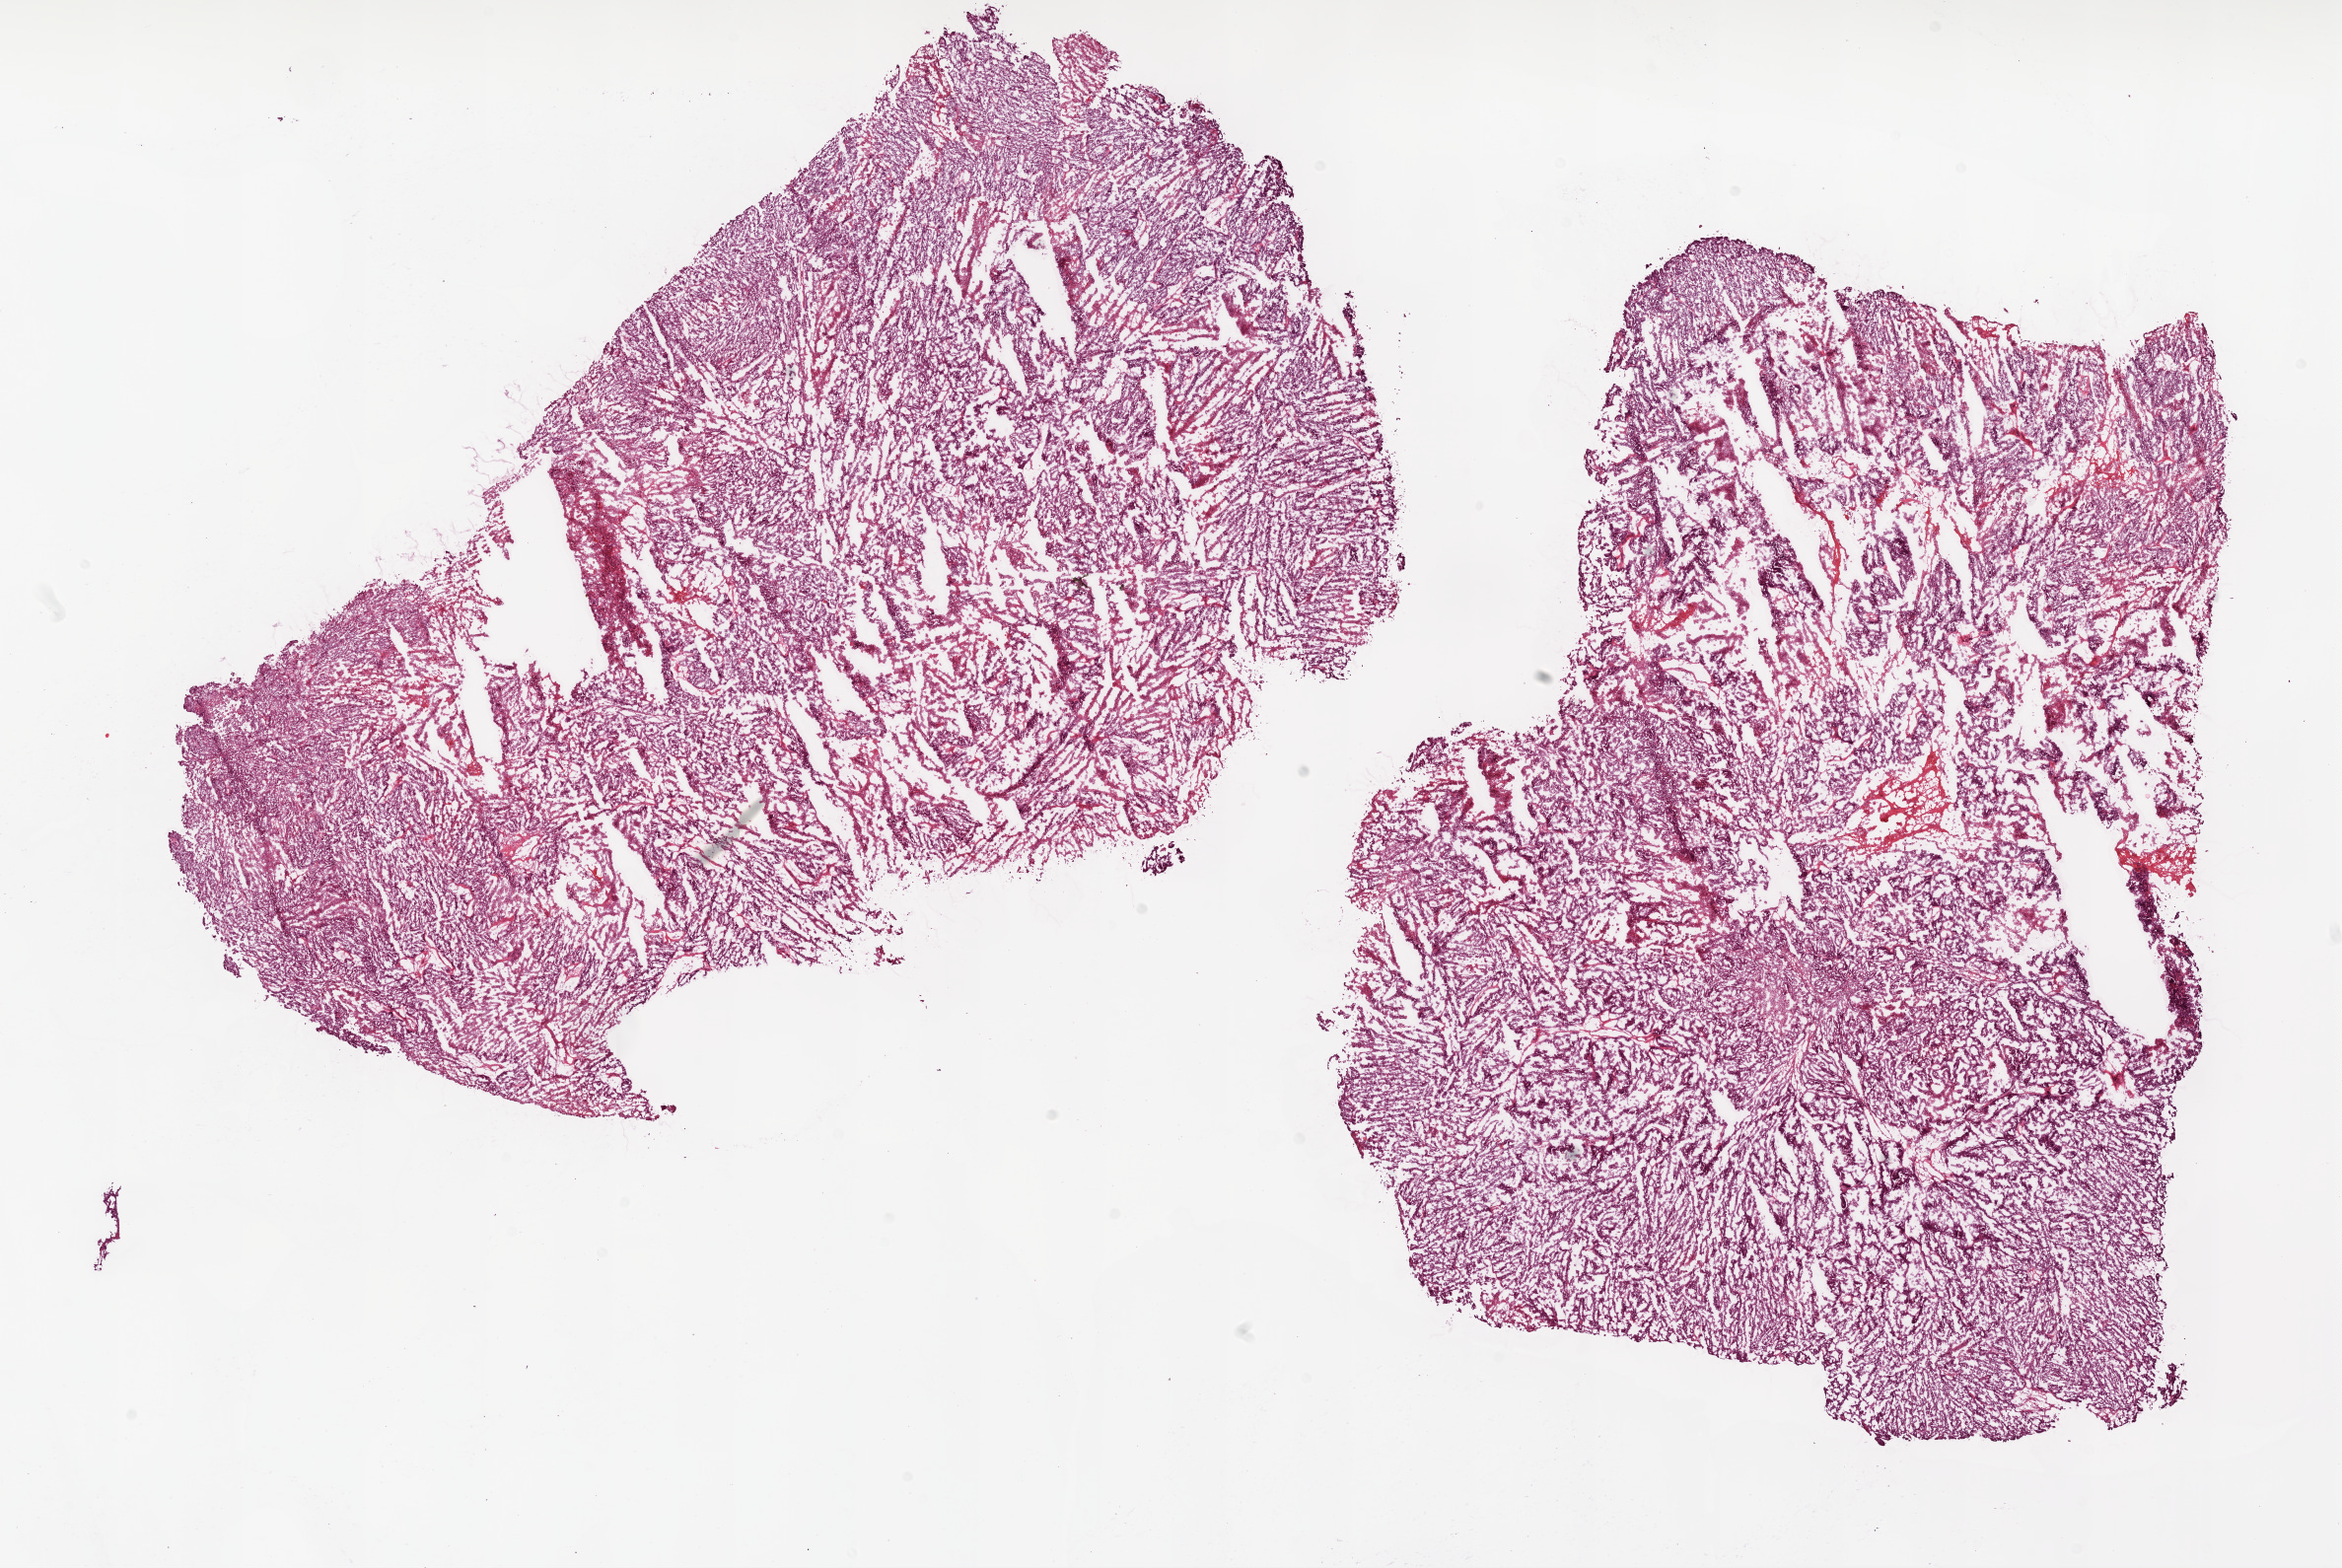
Digitized H&E tissue section (whole slide), a low-resolution overview of the entire scanned area, about 19.1 x 12.8 mm (slide scanned at 20x). Frozen section from the bottom of the tissue portion. Ovary, recurrent tumour sample. Female, age 70 years at initial diagnosis. Slide review estimates, as recorded: tumour cells 90%, tumour nuclei 95%, normal cells 0%, stromal cells 5%, necrosis 5%.
• this section: recurrent tumour
• patient diagnosis: Serous cystadenocarcinoma, NOS